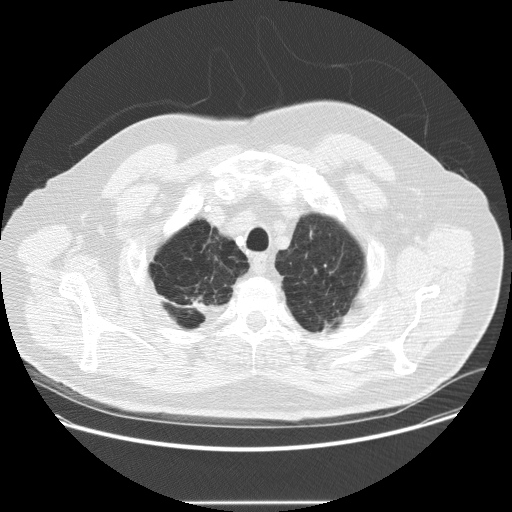
Chest CT (low-dose screening protocol), one axial image. Second annual screen. Lung window (W 1500 / L -600 HU). Slice 47 of 265 in the series. 512 × 512 image matrix. Male participant, aged 64 years at enrolment. Current smoker at enrolment.
- Expert-annotated lung lesion, bounding box (x1, y1, x2, y2) in pixels: (296, 222, 327, 250).
- Screening reader's record for this exam (one nodule recorded; not confirmed to be the boxed lesion): non-calcified nodule or mass ≥4 mm, left upper lobe, 5 × 3 mm, smooth margins, soft tissue attenuation, pre-existing on the prior screen: no.
- Official screen result: positive, other.
- Lung cancer was diagnosed 300 days after this screen: adenocarcinoma, NOS, left upper lobe, poorly differentiated (G3), stage IA (AJCC 6th edition), 8 mm at pathology.